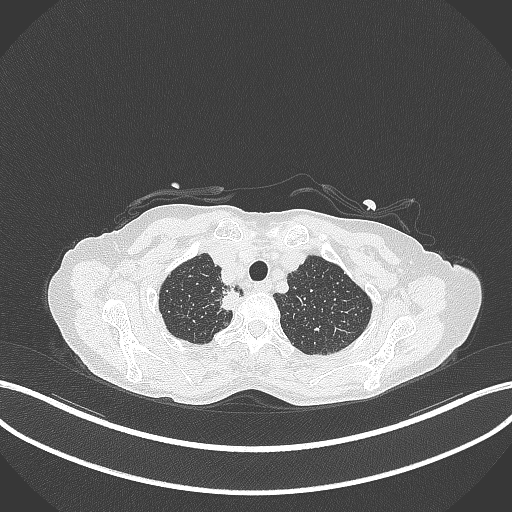
Chest CT, one axial slice; slice 328 of 403 in the series (ordered by position); reconstruction kernel B70f; 120 kVp; lung window (W 1500 / L -600 HU); 1 mm slice thickness; 512 × 512 image matrix. Female patient, age 75 years. Case-level facts recorded for this patient, not image findings: clinical TNM (as recorded): T1c N1 M1.
Outlined on this slice (bounding box drawn by a radiologist):
- lung tumour (recorded histology: adenocarcinoma): bounding box [x1, y1, x2, y2] px = [215, 287, 244, 314]